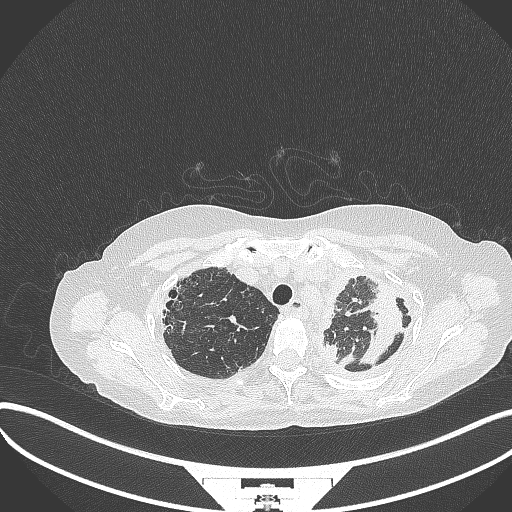
Chest CT, one axial slice. Slice 280 of 373 in the series (ordered by position). Reconstruction kernel B70f. 120 kVp. Lung window (W 1500 / L -600 HU). 512 × 512 image matrix. Patient: female, 56 years. From the clinical record (not read from this slice): clinical TNM (as recorded): T1 N0 M0.
Annotated regions visible in this slice (bounding box drawn by a radiologist):
- lung tumour (recorded histology: adenocarcinoma): bounding box (x1, y1, x2, y2) in pixels: (350, 288, 408, 371)